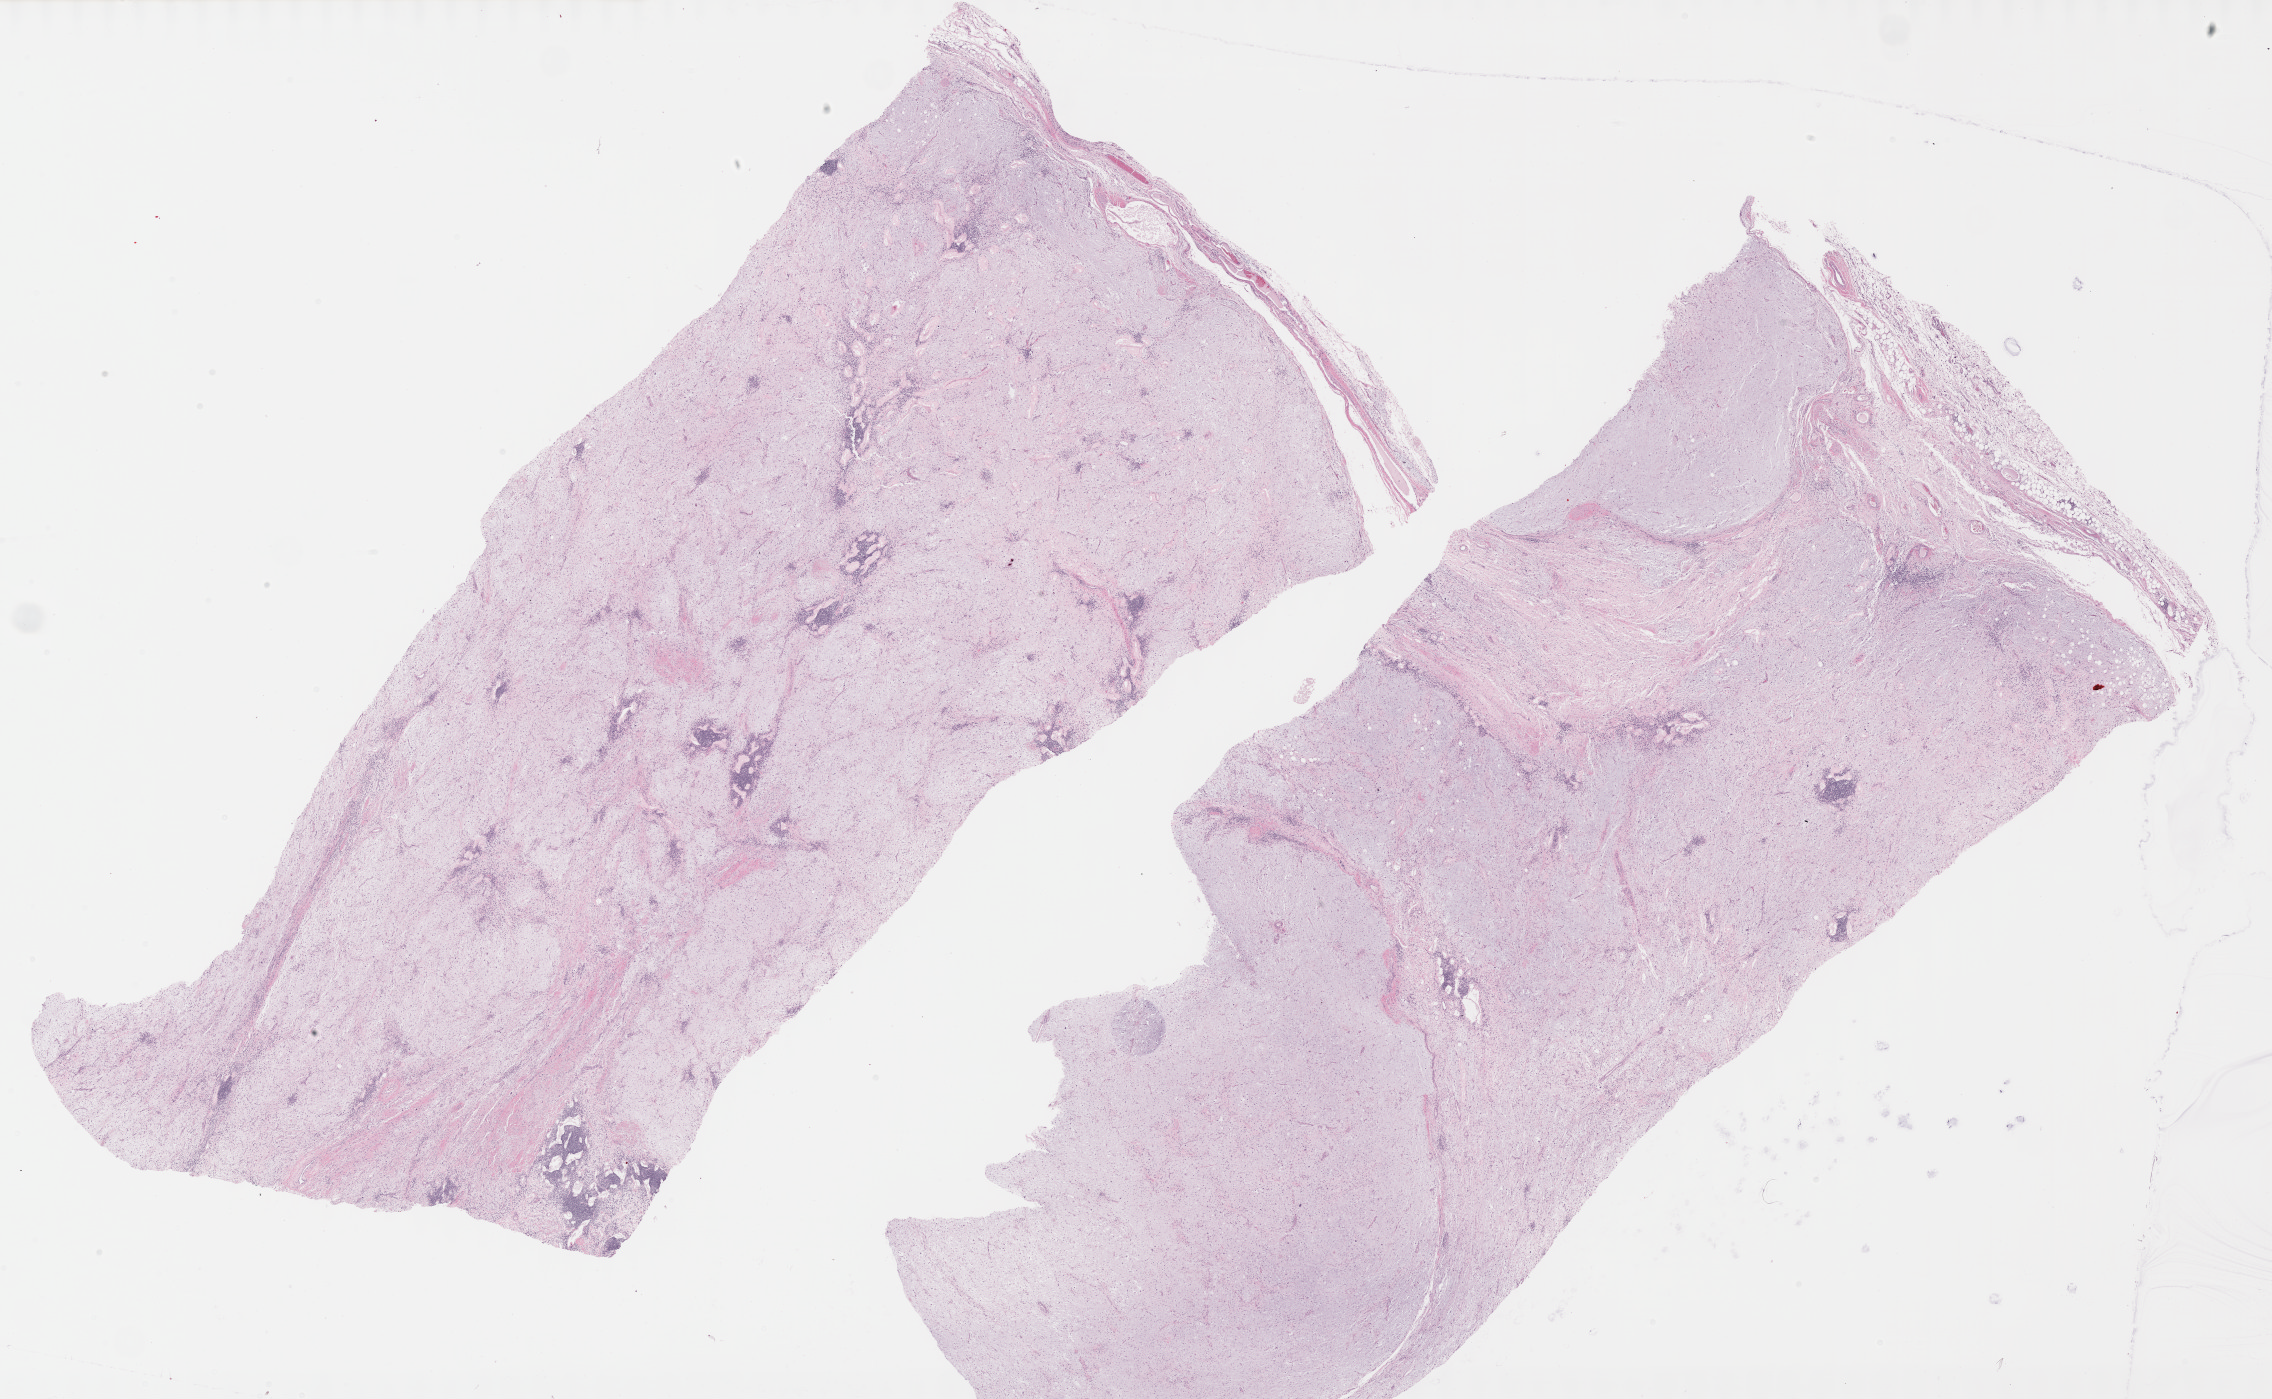
Hematoxylin and eosin (H&E) stained whole-slide image, low-resolution overview of the scanned area, about 36.7 x 22.6 mm (from a 40x scan), formalin-fixed paraffin-embedded (FFPE) diagnostic section, retroperitoneum and peritoneum, primary tumour sample. Female, age 50 years at initial diagnosis.
Pathologic diagnosis: Dedifferentiated liposarcoma (retroperitoneum).